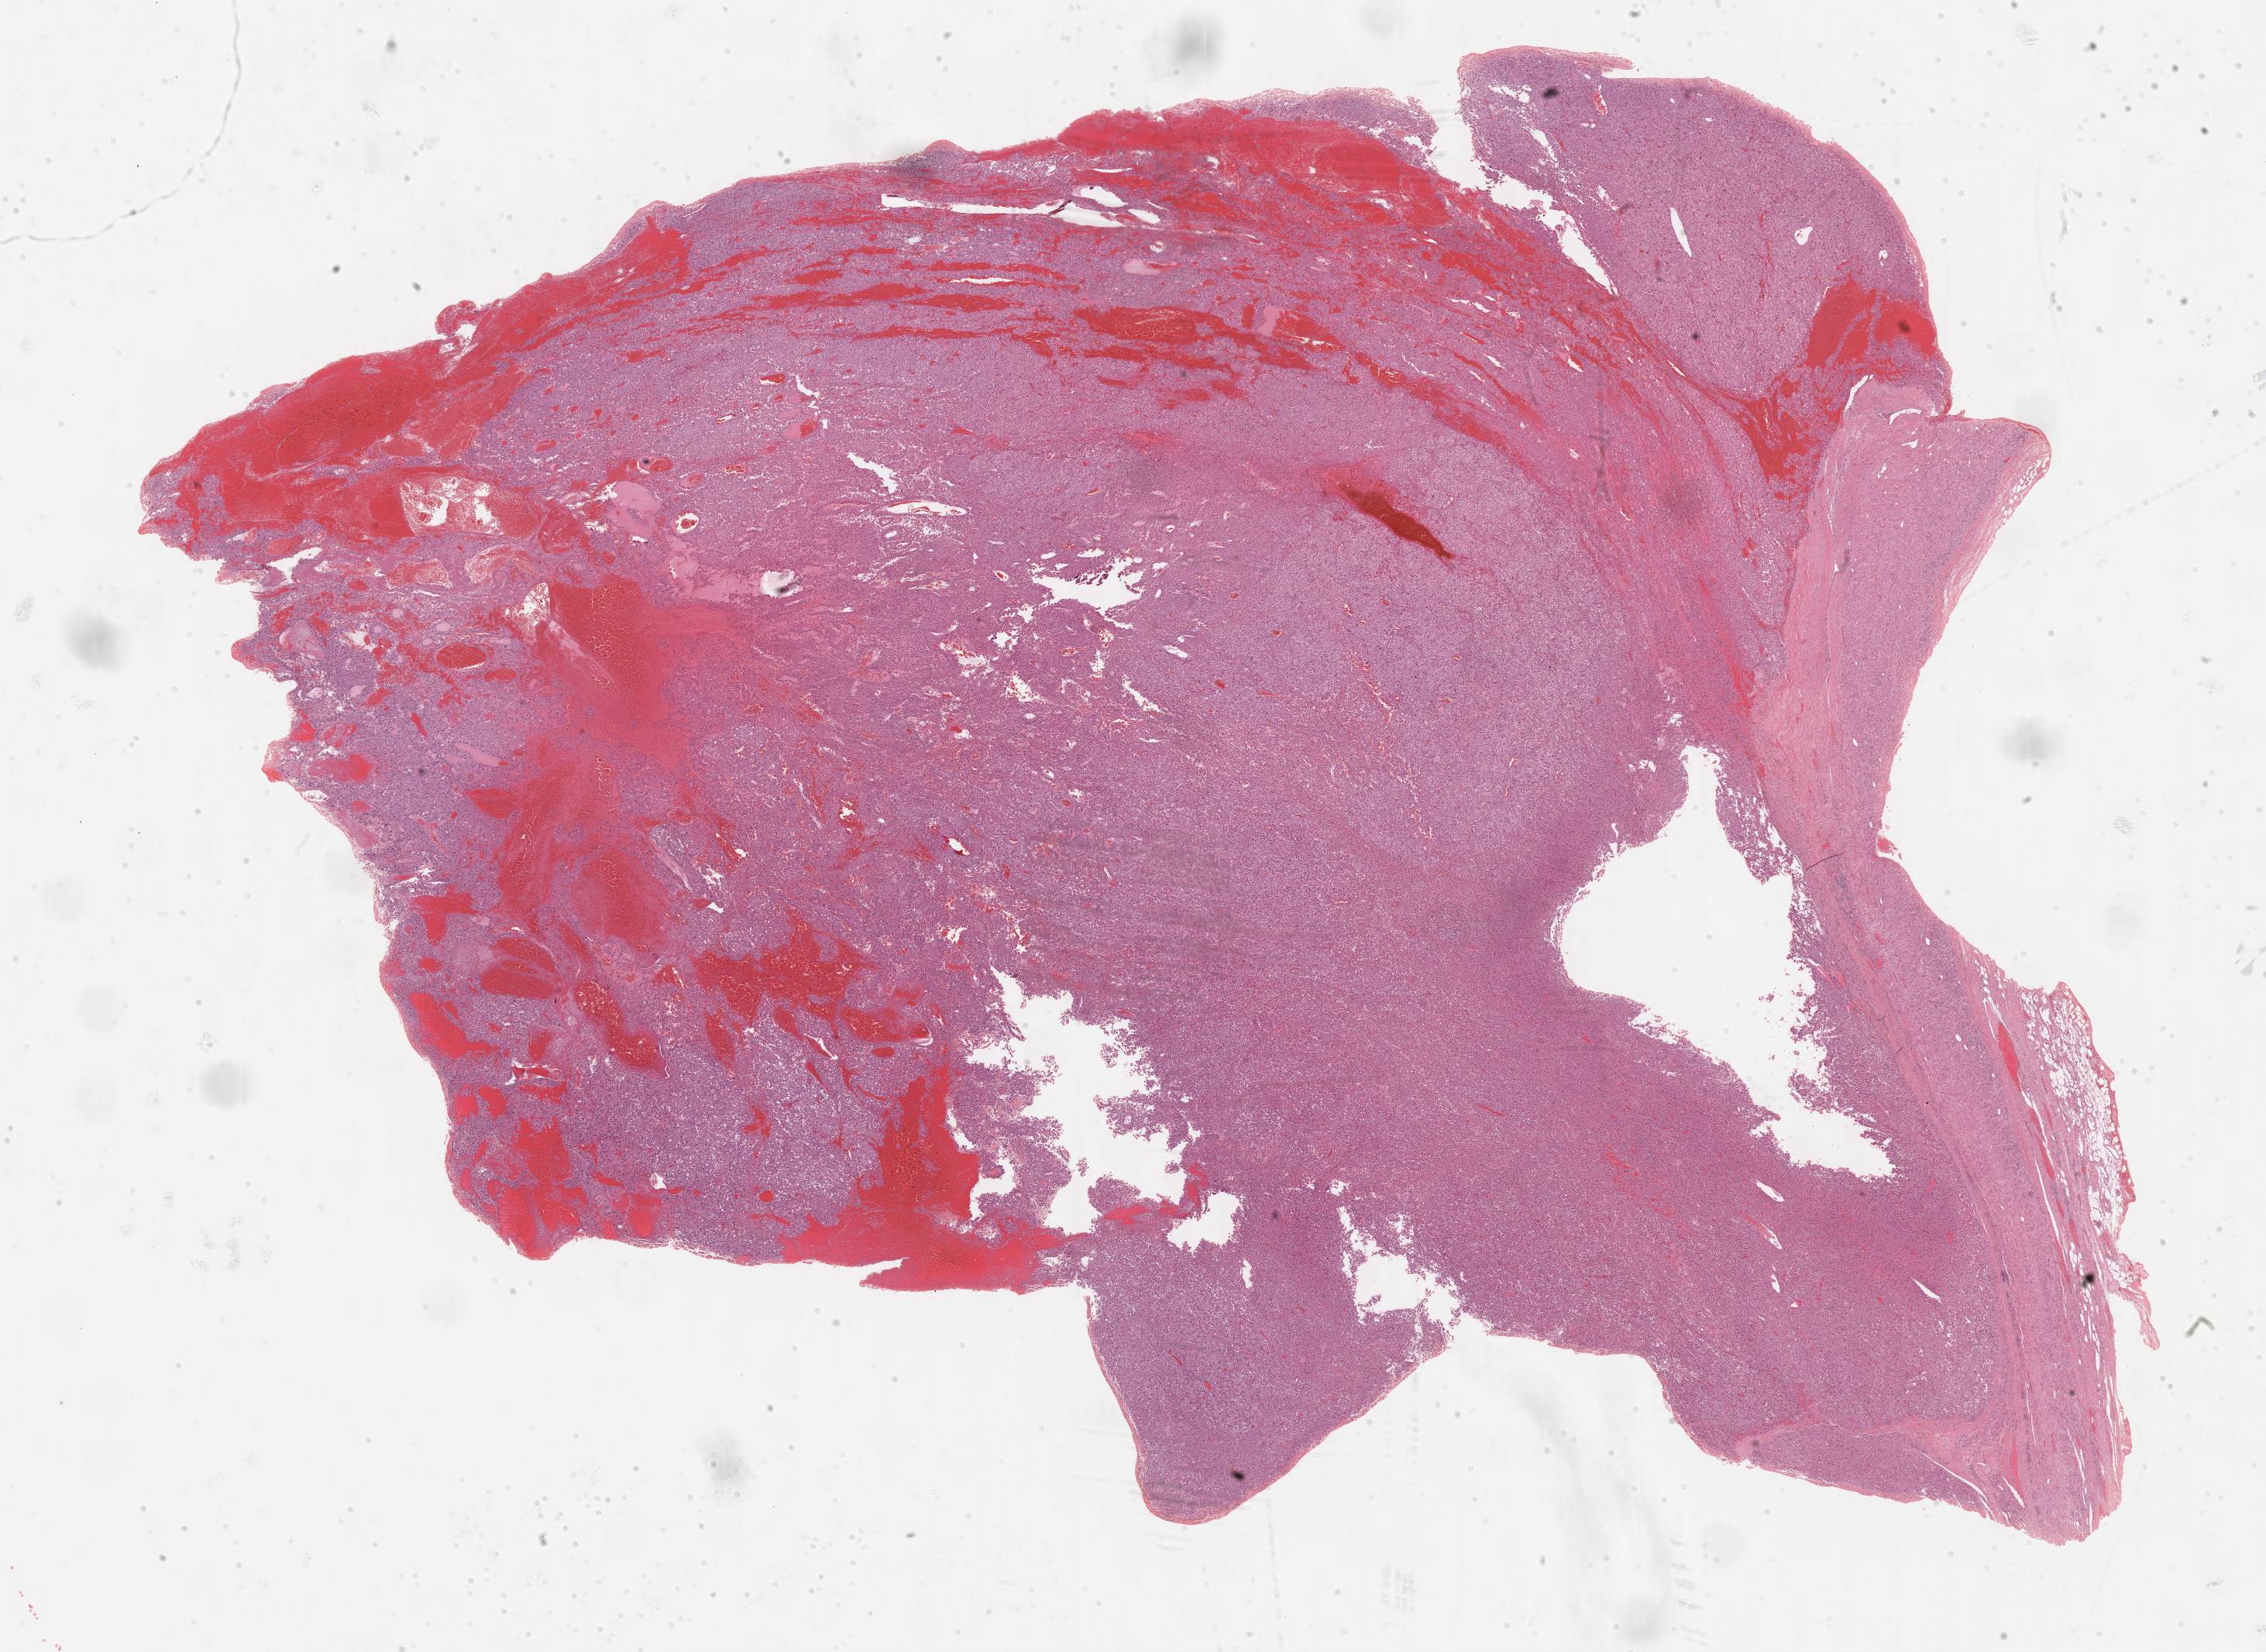
Digitized H&E tissue section (whole slide), shown as a low-resolution overview of the whole scanned area (about 23.7 x 17.3 mm). Formalin-fixed paraffin-embedded (FFPE) diagnostic section. Primary tumour sample from the adrenal cortex. Male patient; age at initial diagnosis 53 years.
Laterality: left. Pathologic diagnosis: Adrenal cortical carcinoma (cortex of adrenal gland).